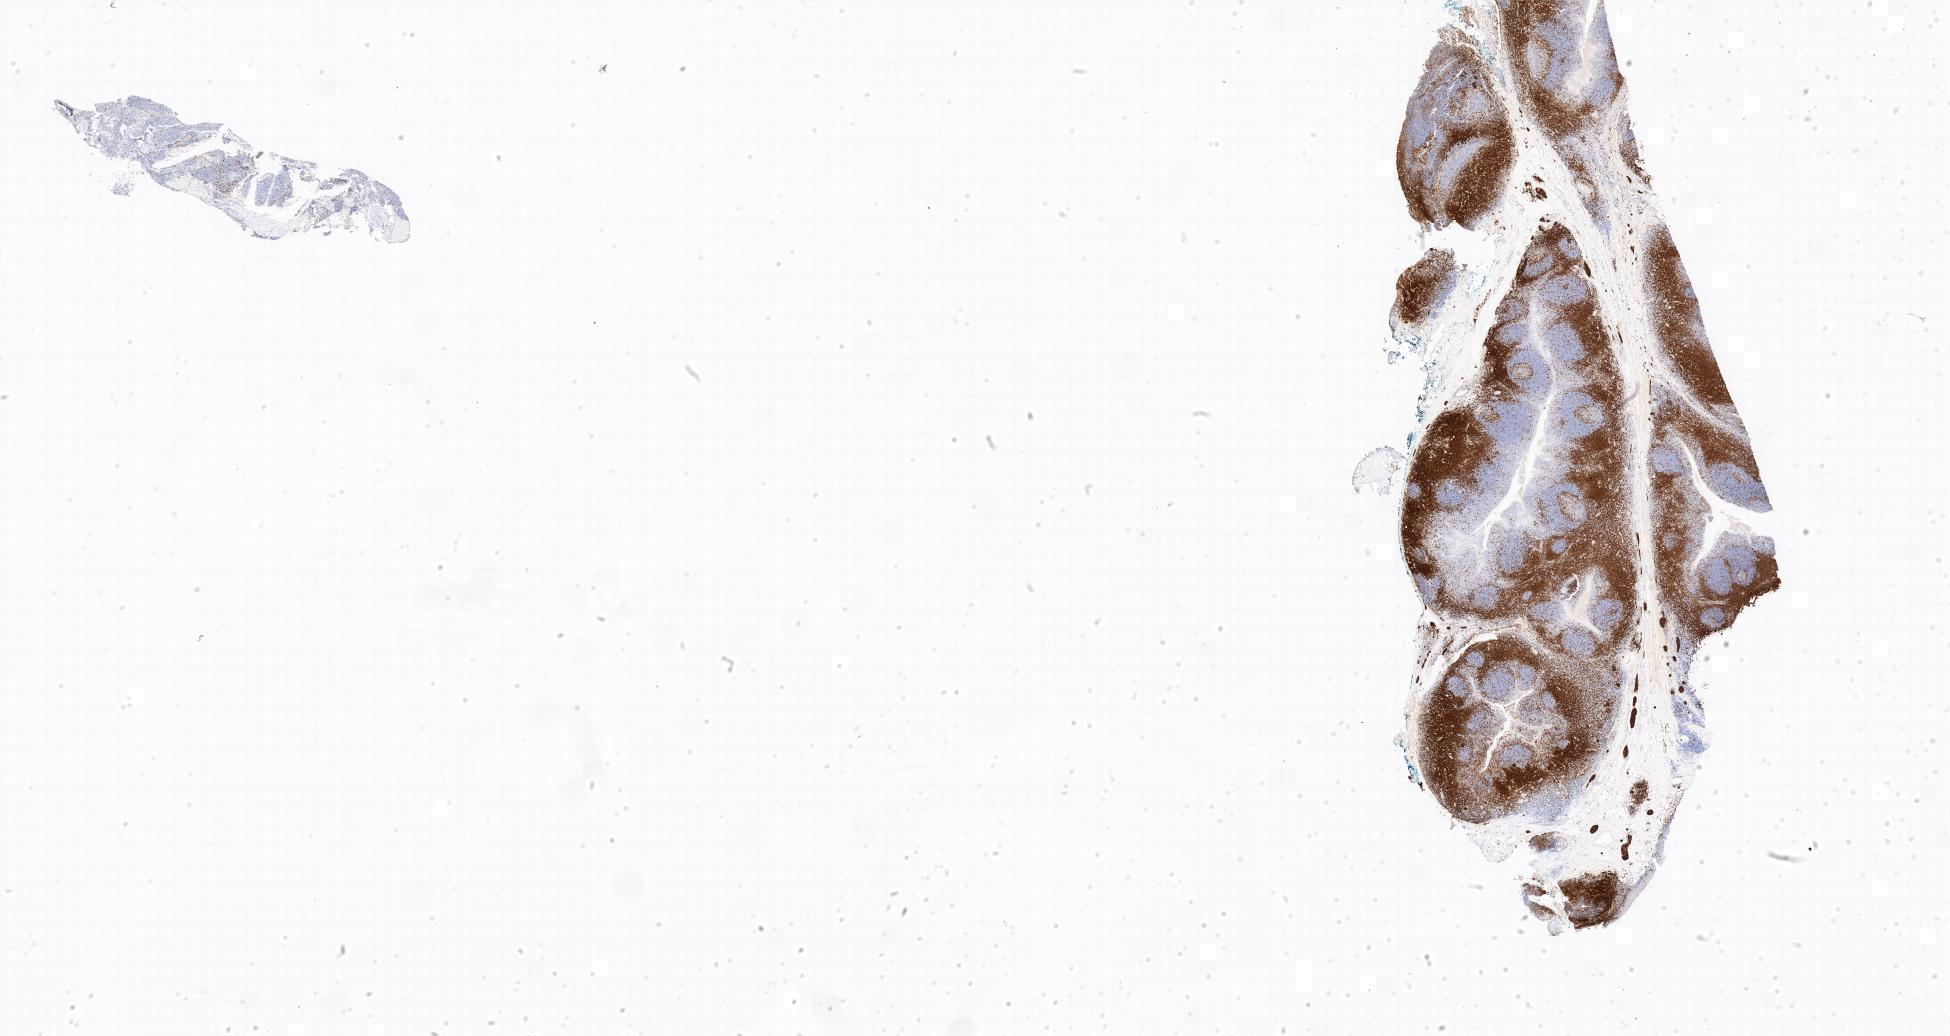
IHC for CD3, whole-slide image, shown as a low-resolution overview of the whole scanned area, tumor tissue, anatomic site: bone marrow. Female, age 3 years at initial diagnosis.
• diagnosis: Burkitt lymphoma, NOS